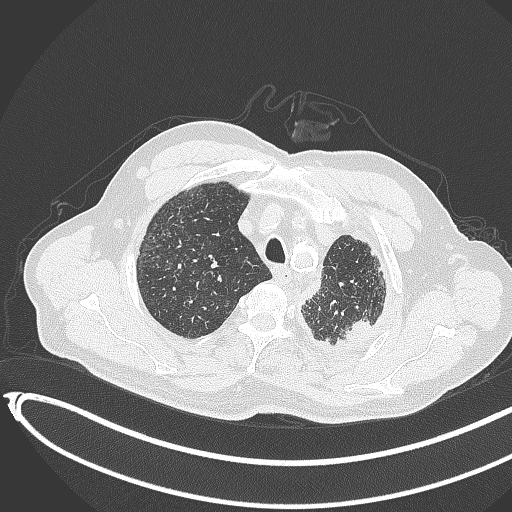
Chest CT, one axial slice. Position 359 of 451 along the scan axis. Reconstruction kernel B70f. 120 kVp. Lung window (W 1500 / L -600 HU). 1 mm slice thickness. 512 × 512 image matrix, field of view 400 × 400 mm. Male patient, age 78 years. Case-level facts recorded for this patient, not image findings: clinical TNM (as recorded): T1c N0 M1.
Structures marked on this image (bounding box drawn by a radiologist):
- lung tumour (recorded histology: adenocarcinoma): box from (x=336, y=311) to (x=373, y=347) px